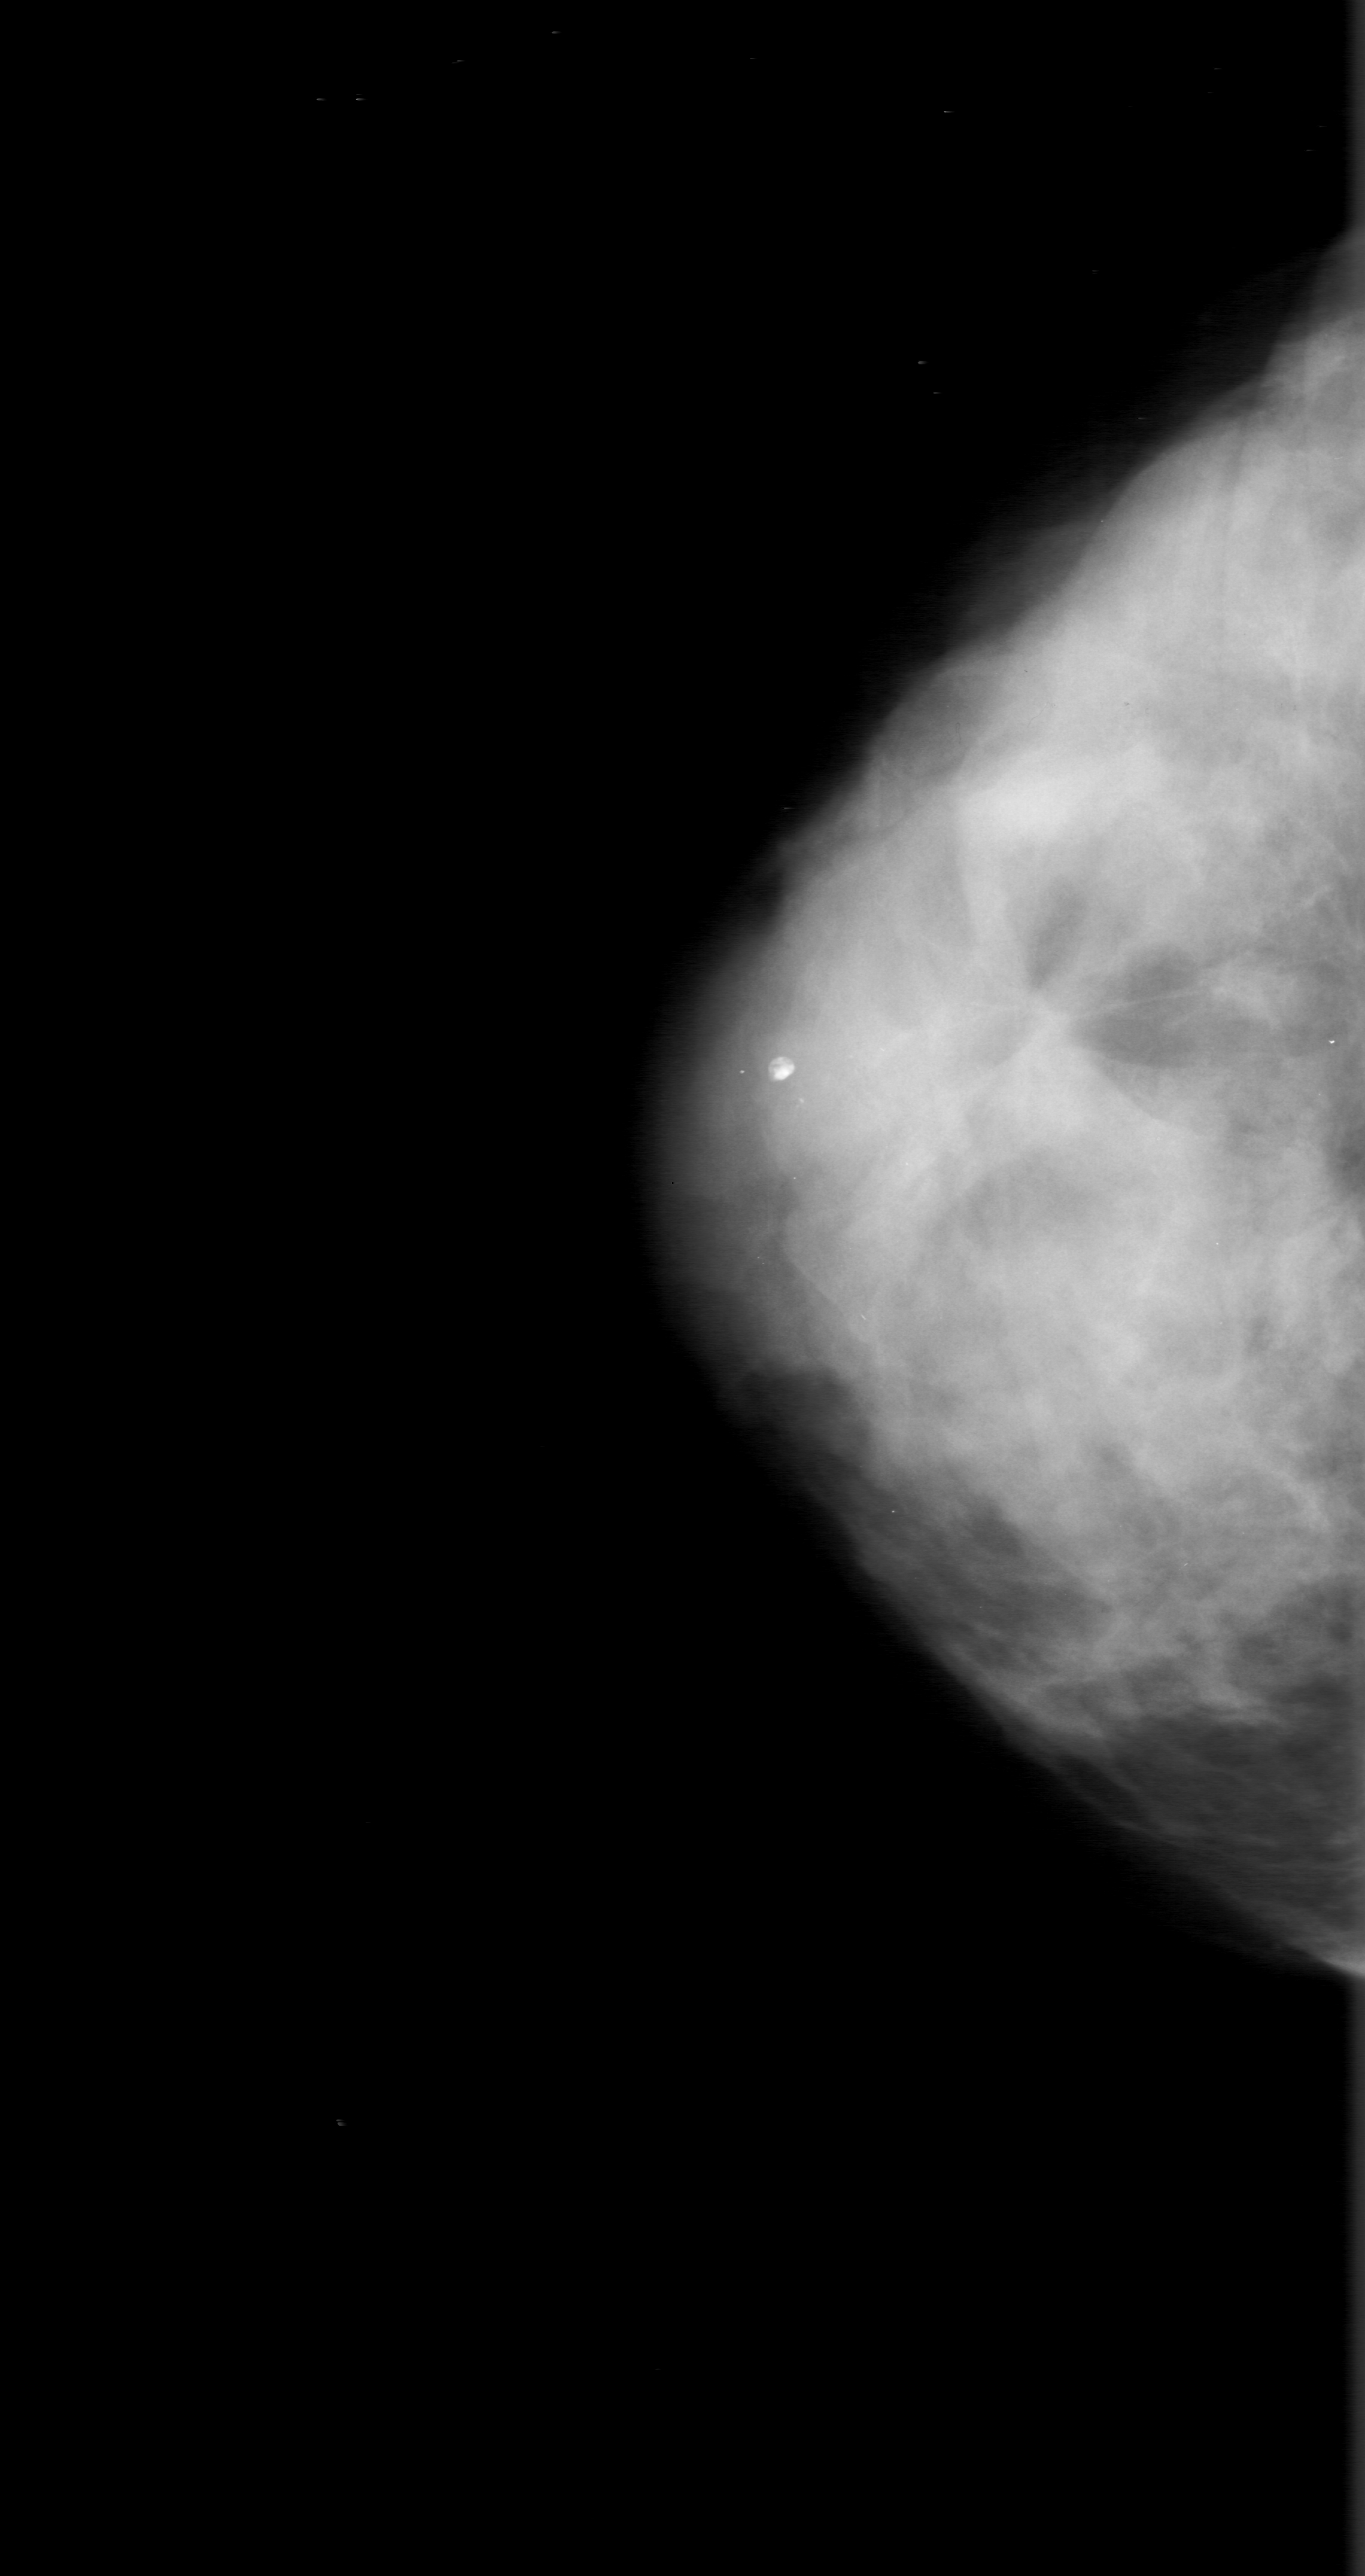
Scanned film-screen mammogram, right breast, CC view.
Abnormality record for this image: mass, shape architectural distortion; BI-RADS assessment category 5; subtlety rating 4 on a 1 (subtle) to 5 (obvious) scale; pathology (as recorded): malignant.